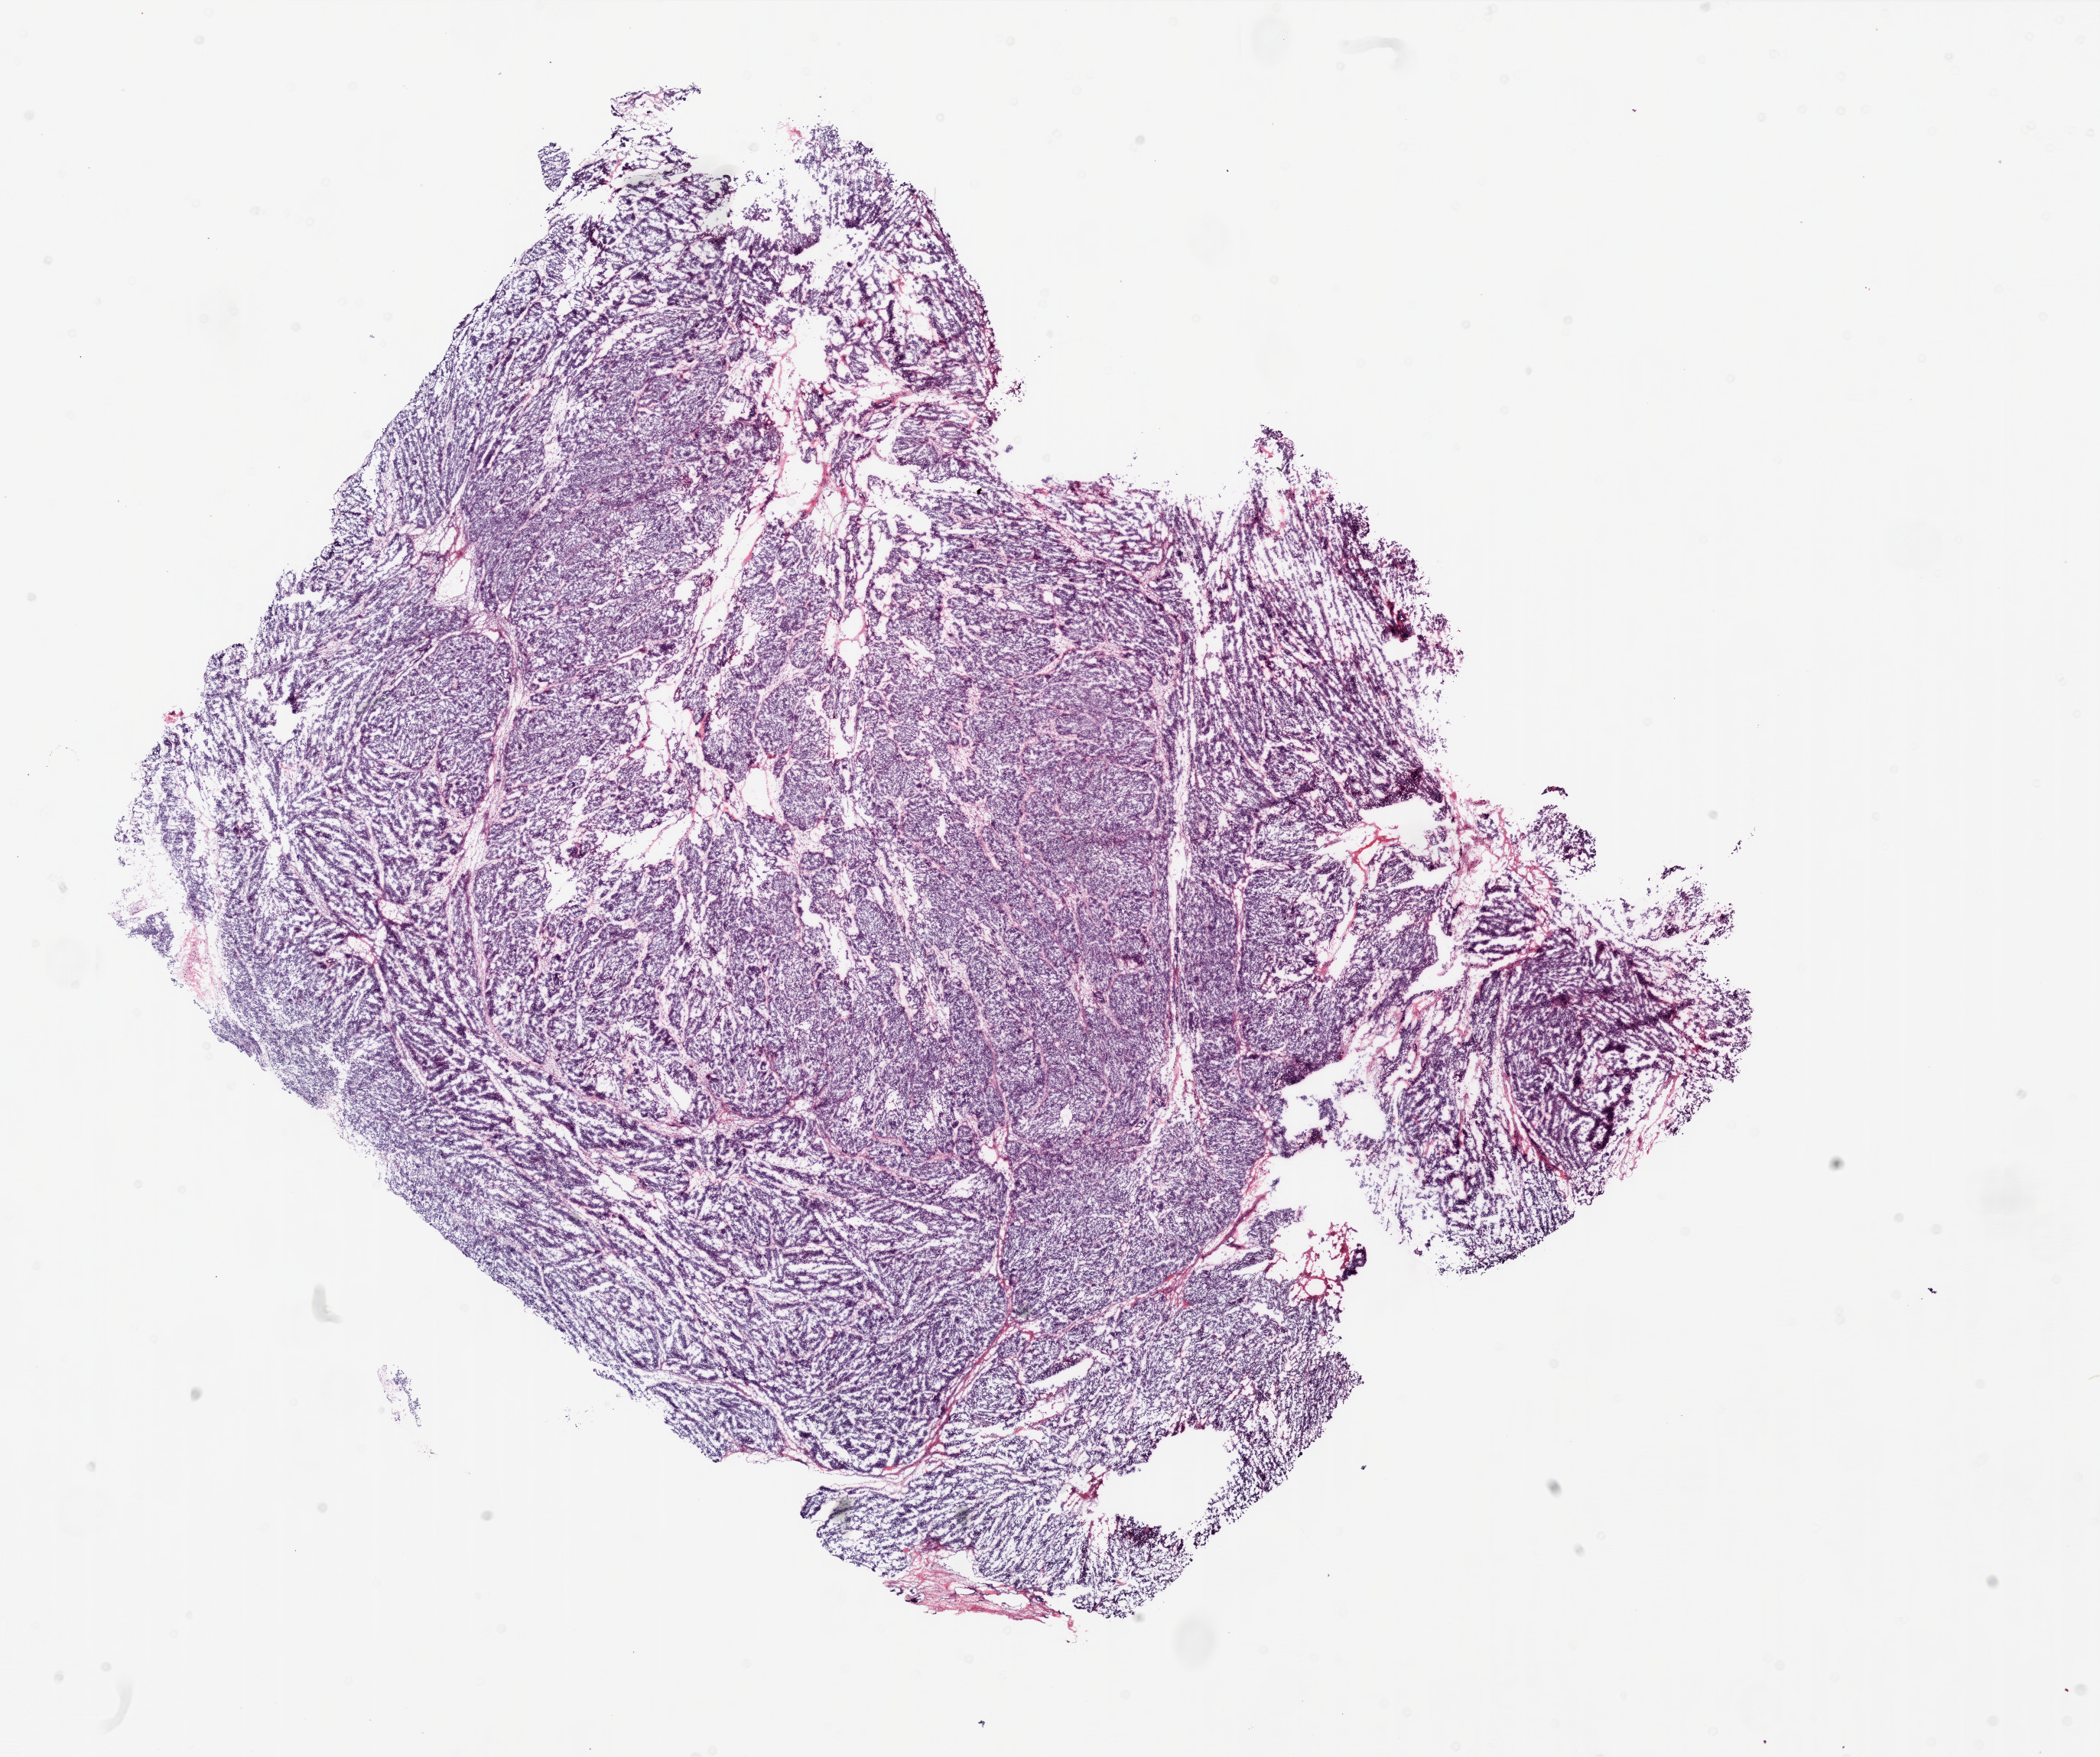
Digitized Hematoxylin and eosin (H&E) stained tissue section (whole slide), shown as a low-resolution overview of the whole scanned area (about 22.0 x 18.4 mm, acquisition: 20x scan), frozen section, ovary, primary tumour sample. Female, age 72 years at initial diagnosis. Histologic grade: G3 (poorly differentiated). Slide review estimates, as recorded: tumour cells 95%, tumour nuclei 98%, normal cells 0%, stromal cells 5%, necrosis 0%.
- diagnosis: Serous cystadenocarcinoma, NOS
- FIGO stage: IIIC